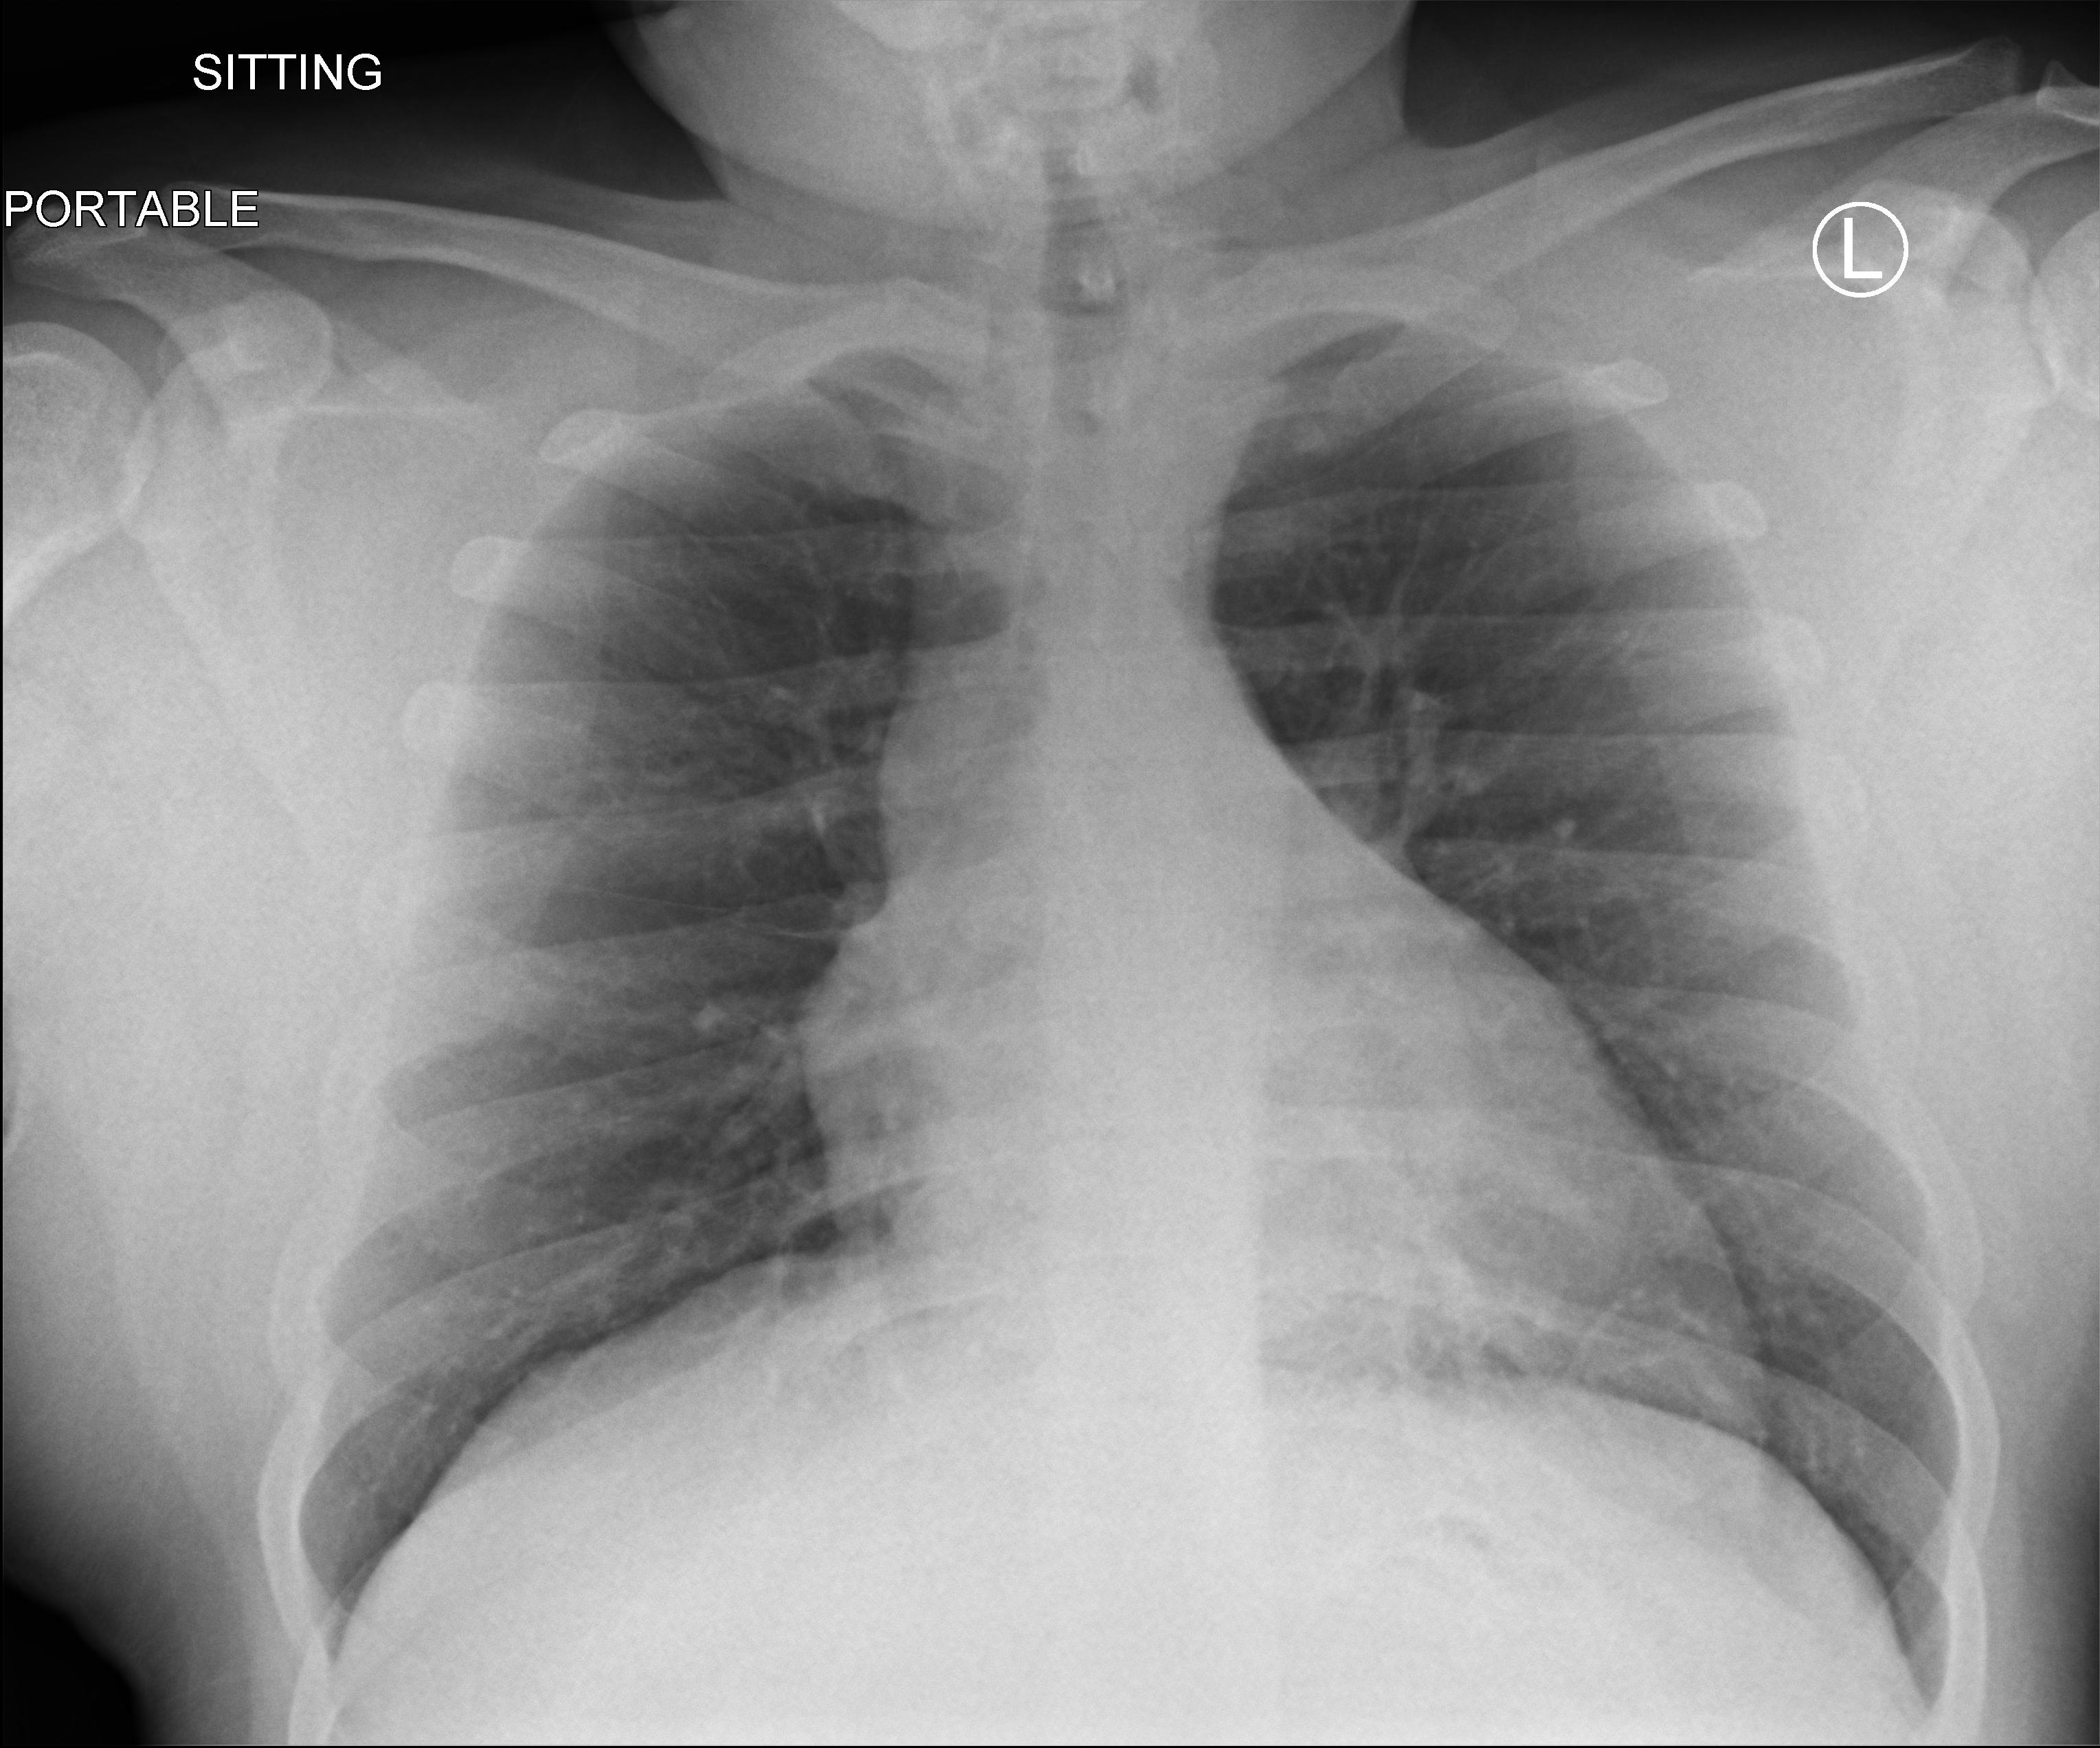
Chest X-ray (portable), anteroposterior (AP) projection. Patient hospitalised with COVID-19; female, aged 18–59 years.
From the hospital-stay record, not from the radiograph (when in the stay this image was taken is not recorded):
- admitted to intensive care during this hospital stay: no
- mechanically ventilated during this hospital stay: no